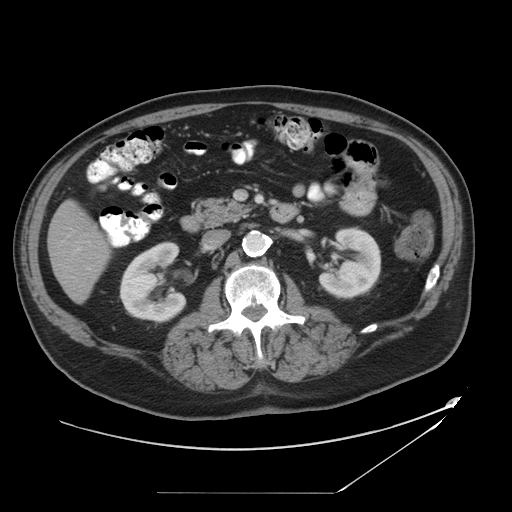
Contrast-enhanced abdominal CT, one axial slice; position 16 of 49 along the scan axis; reconstruction kernel STANDARD; 120 kVp; intravenous contrast given; soft-tissue window (W 400 / L 40 HU); 5 mm slice thickness; 512 × 512 image matrix. Male patient, age 72 years. From the clinical record (not read from this slice): diagnosis: colorectal cancer liver metastases, imaged before liver resection; multiple liver metastases: no; largest metastasis: 2.5 cm; disease in both lobes: no.
Outlined on this slice (outlined manually by an expert reader):
- liver: bounding box <49,203,110,301> (left, top, right, bottom; pixels)
- planned liver remnant (the part of the liver to remain after resection): <49,203,110,301>